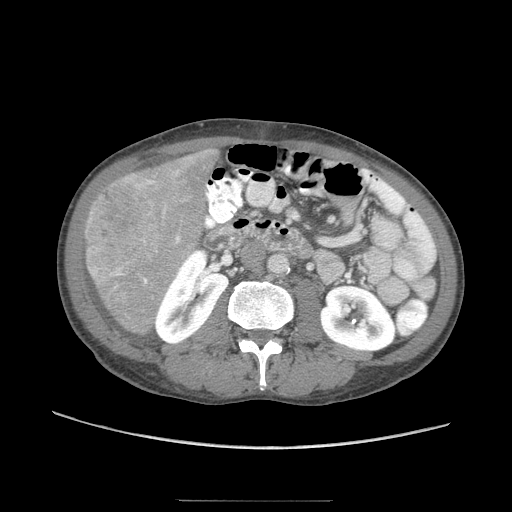
Contrast-enhanced abdominal CT (liver protocol), one axial slice; slice 18 of 103 in the series (ordered by position); reconstruction kernel STANDARD; soft-tissue window (W 400 / L 40 HU); 2.5 mm slice thickness; 512 × 512 image matrix, field of view 380 × 380 mm. Case-level facts recorded for this patient, not image findings: diagnosis: hepatocellular carcinoma (patient treated with transarterial chemoembolisation; whether this scan precedes or follows treatment is not stated here); TNM stage (as recorded): Stage-IIIA; Child-Pugh class: A; tumour nodularity: multinodular; tumour size: 16 cm.
Annotated regions visible in this slice (semi-automatic segmentation, software-assisted and operator-edited):
- liver parenchyma outside the tumour (the mass and vessels are separate outlines, so this box may not span the whole liver): box from (x=84, y=148) to (x=220, y=332) px
- mass: (x=84, y=164)–(x=170, y=307)
- liver vessels: (x=162, y=226)–(x=167, y=238)